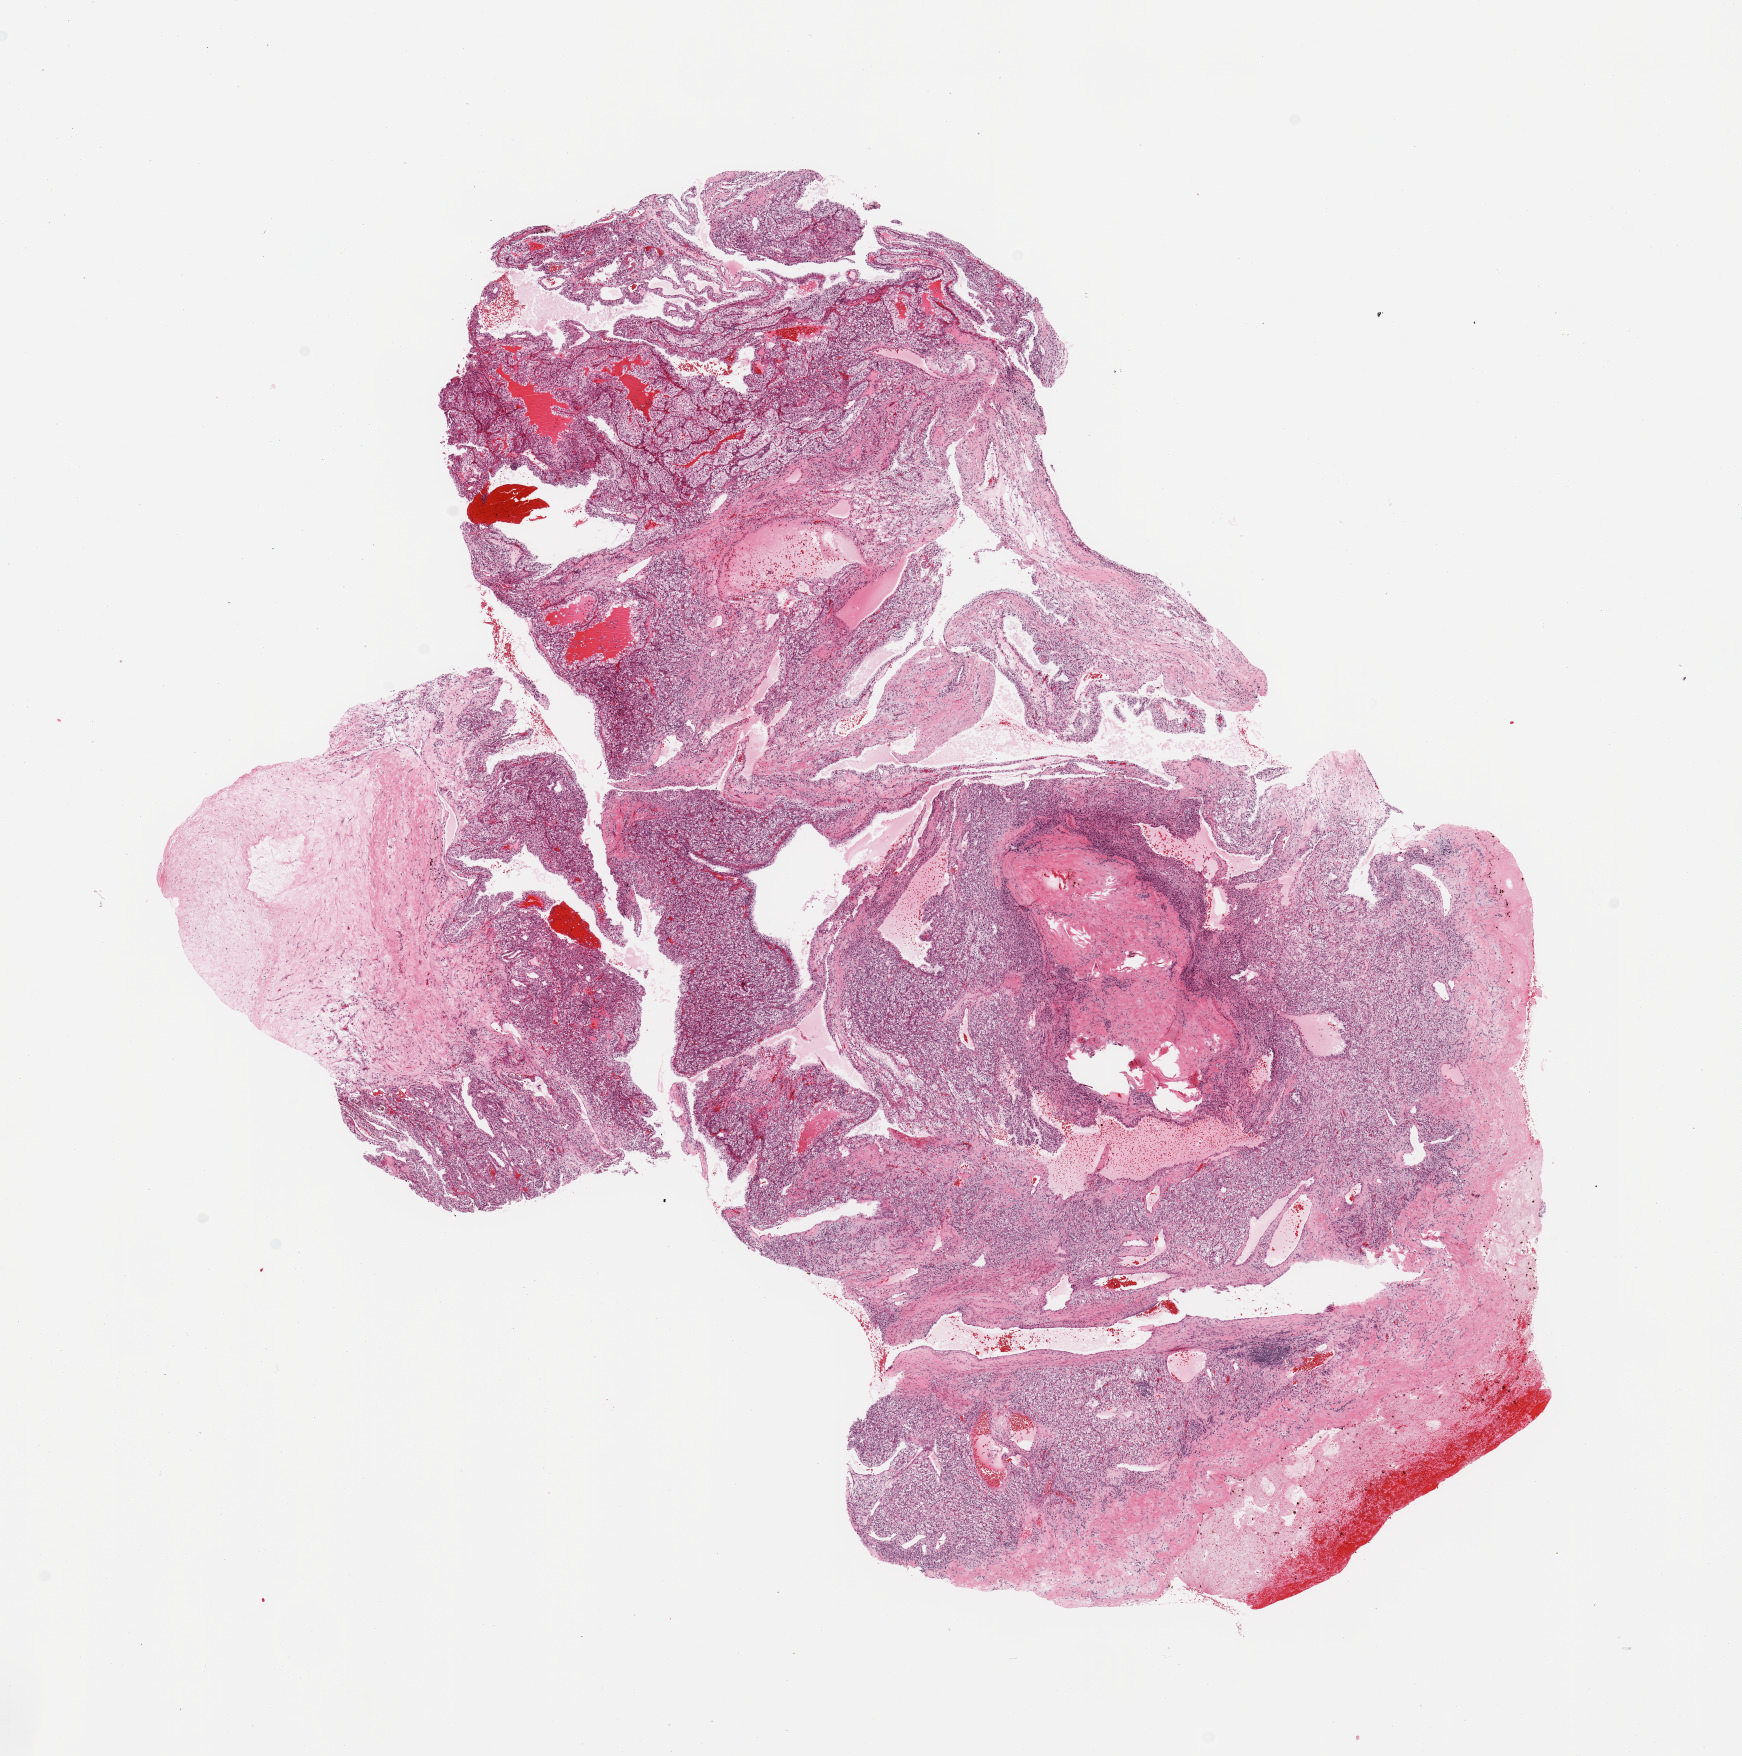
H&E-stained whole-slide image — low-resolution overview of the scanned area, about 13.8 x 13.9 mm (from a 20x scan); tumour tissue sample, sampled site: kidney. Patient: male, age 30 years.
Diagnosis: Renal cell carcinoma, NOS.